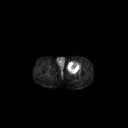
FDG PET of an extremity soft-tissue mass (from a PET/CT study), one axial slice. Position 259 of 267 along the scan axis. 128 × 128 image matrix, field of view 700 × 700 mm. Male patient, age 63 years. Case-level facts recorded for this patient, not image findings: histological type: pleiomorphic liposarcoma; grade: high; site of the primary tumour: left thigh.
Outlined on this slice (expert contour drawn on MRI and transferred to this co-registered scan by the dataset authors):
- gross tumour volume including surrounding oedema: bounding box (x1, y1, x2, y2) in pixels: (67, 61, 80, 72)
- gross tumour volume (mass): (67, 62, 79, 71)